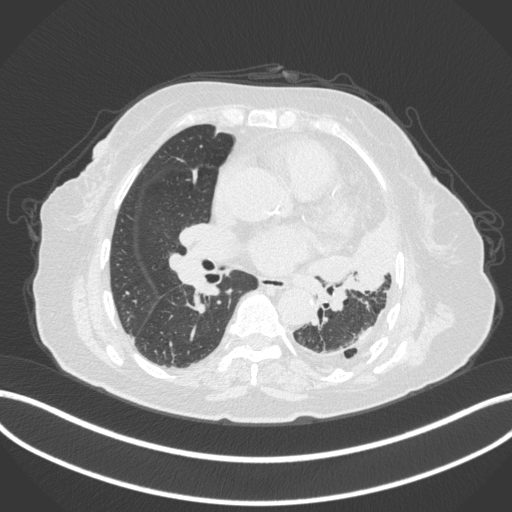
Chest CT, one axial slice; slice 186 of 399 in the series (ordered by position); 120 kVp; lung window (W 1500 / L -600 HU); 1 mm slice thickness; 512 × 512 image matrix. Female patient, age 75 years. Case-level facts recorded for this patient, not image findings: clinical TNM (as recorded): T3 N3 M1.
Outlined on this slice (bounding box drawn by a radiologist):
- lung tumour (recorded histology: adenocarcinoma): bounding box <297,220,401,298> (left, top, right, bottom; pixels)